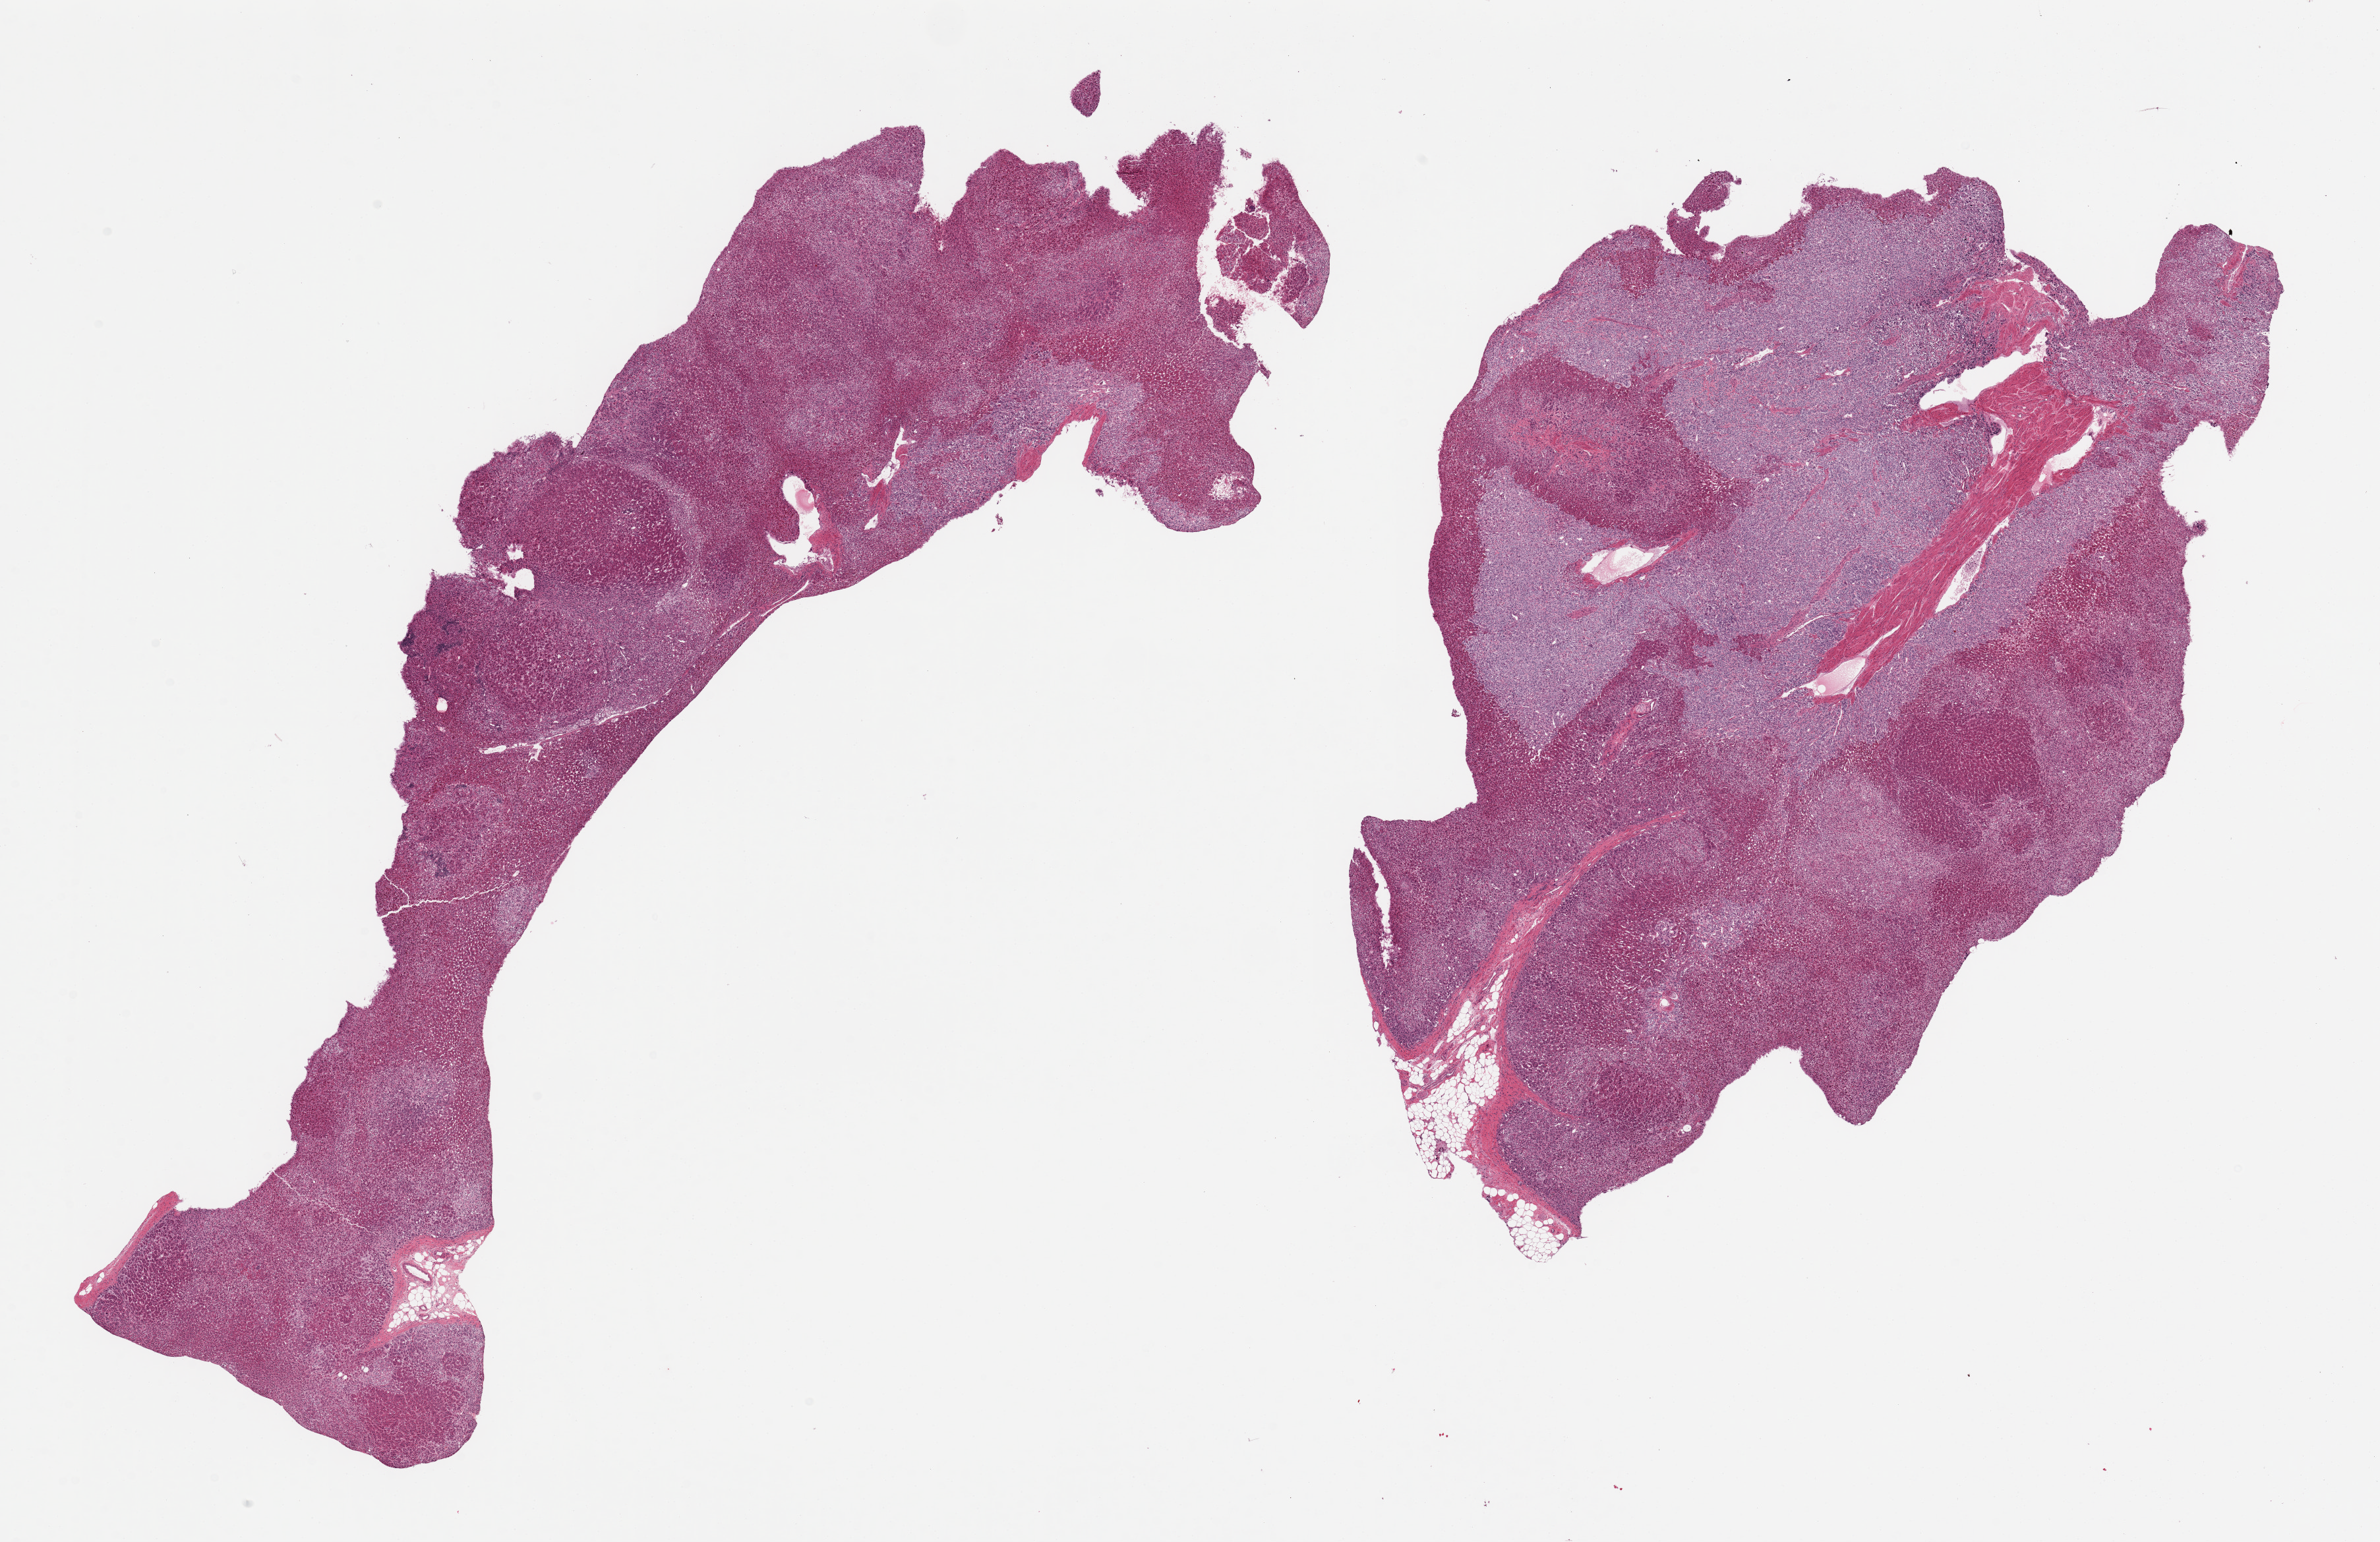
Digitized hematoxylin and eosin (H&E)-stained section, brightfield, shown as a low-resolution overview of the whole scanned area (about 28.5 x 18.5 mm). PAXgene-fixed, paraffin-embedded tissue. Section of adrenal gland (target tissue). Tissue donor sample. Male donor.
Review note (as recorded): 2 pieces.Medullary hyperplasia: abundant (80%) medulla especially in one piece; could account for patient's hypertension.